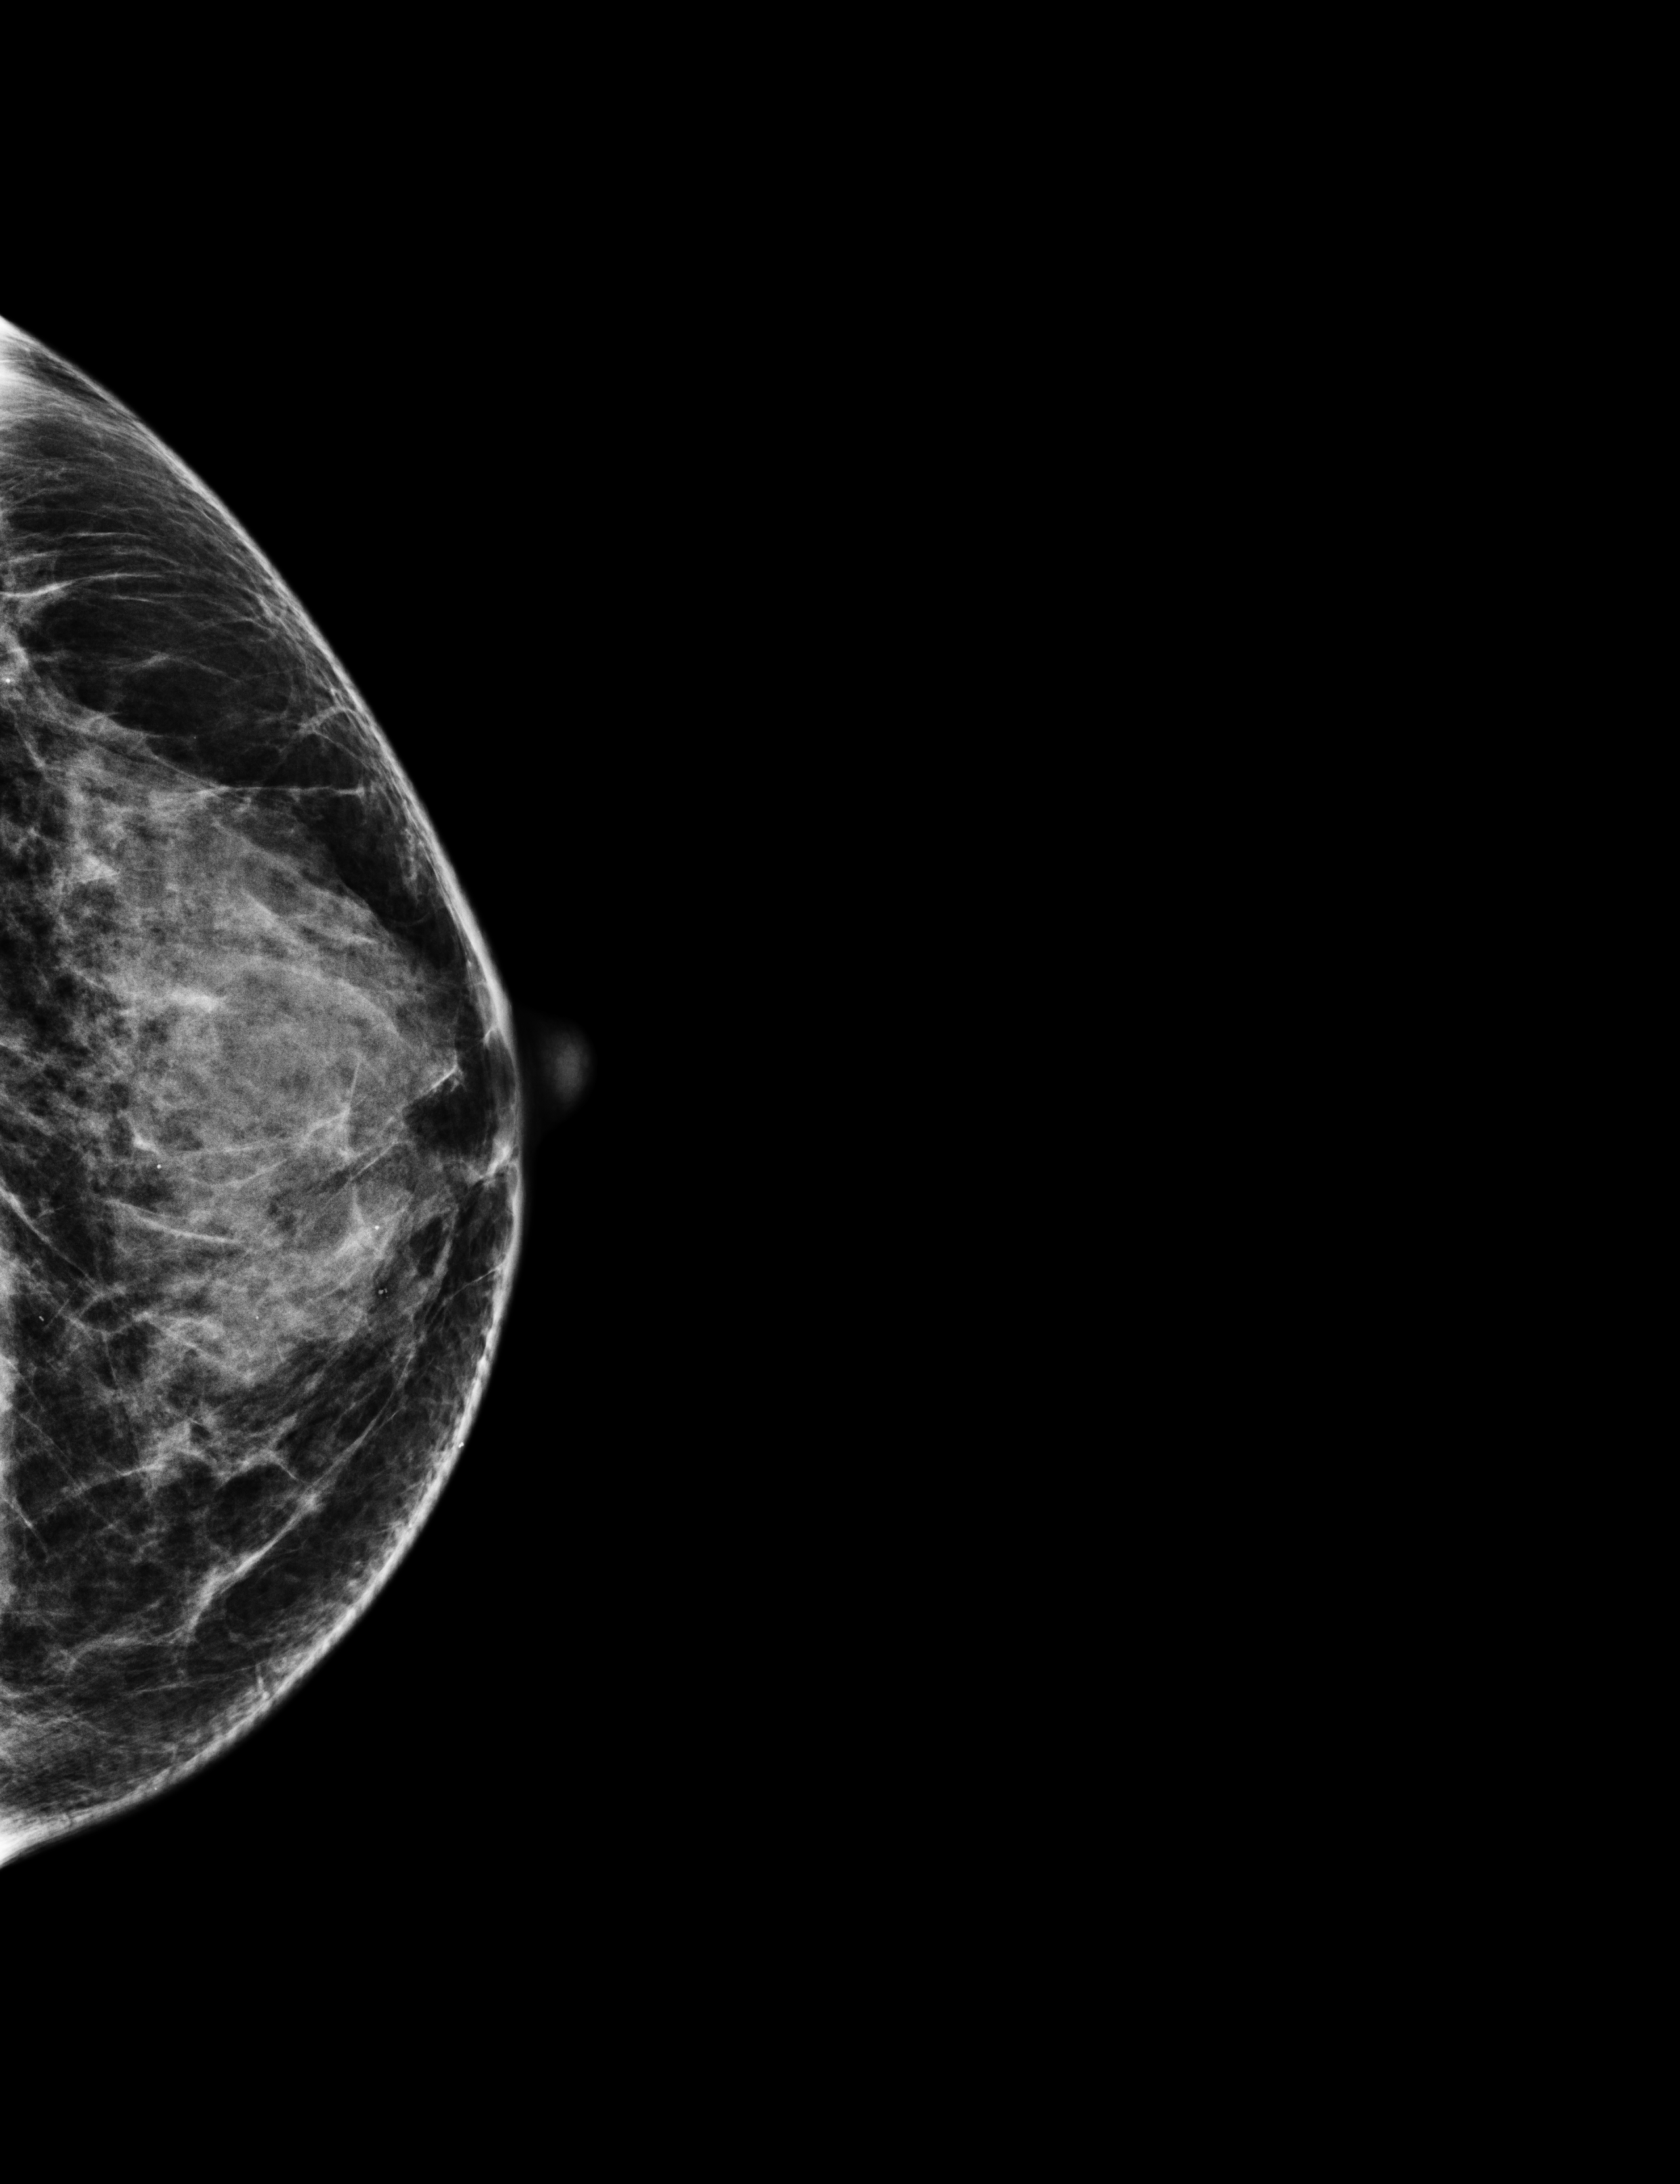
Screening examination; compressed breast thickness 45 mm. Female patient, age 55 years.
Image type: full-field digital mammogram. Breast: left. Projection: CC view. BI-RADS breast density category at the screening exam (both breasts, scale 1–4): 3. Final BI-RADS category for the screening round (tomosynthesis exam, both breasts): category 1. Recall: no recall after this screen.